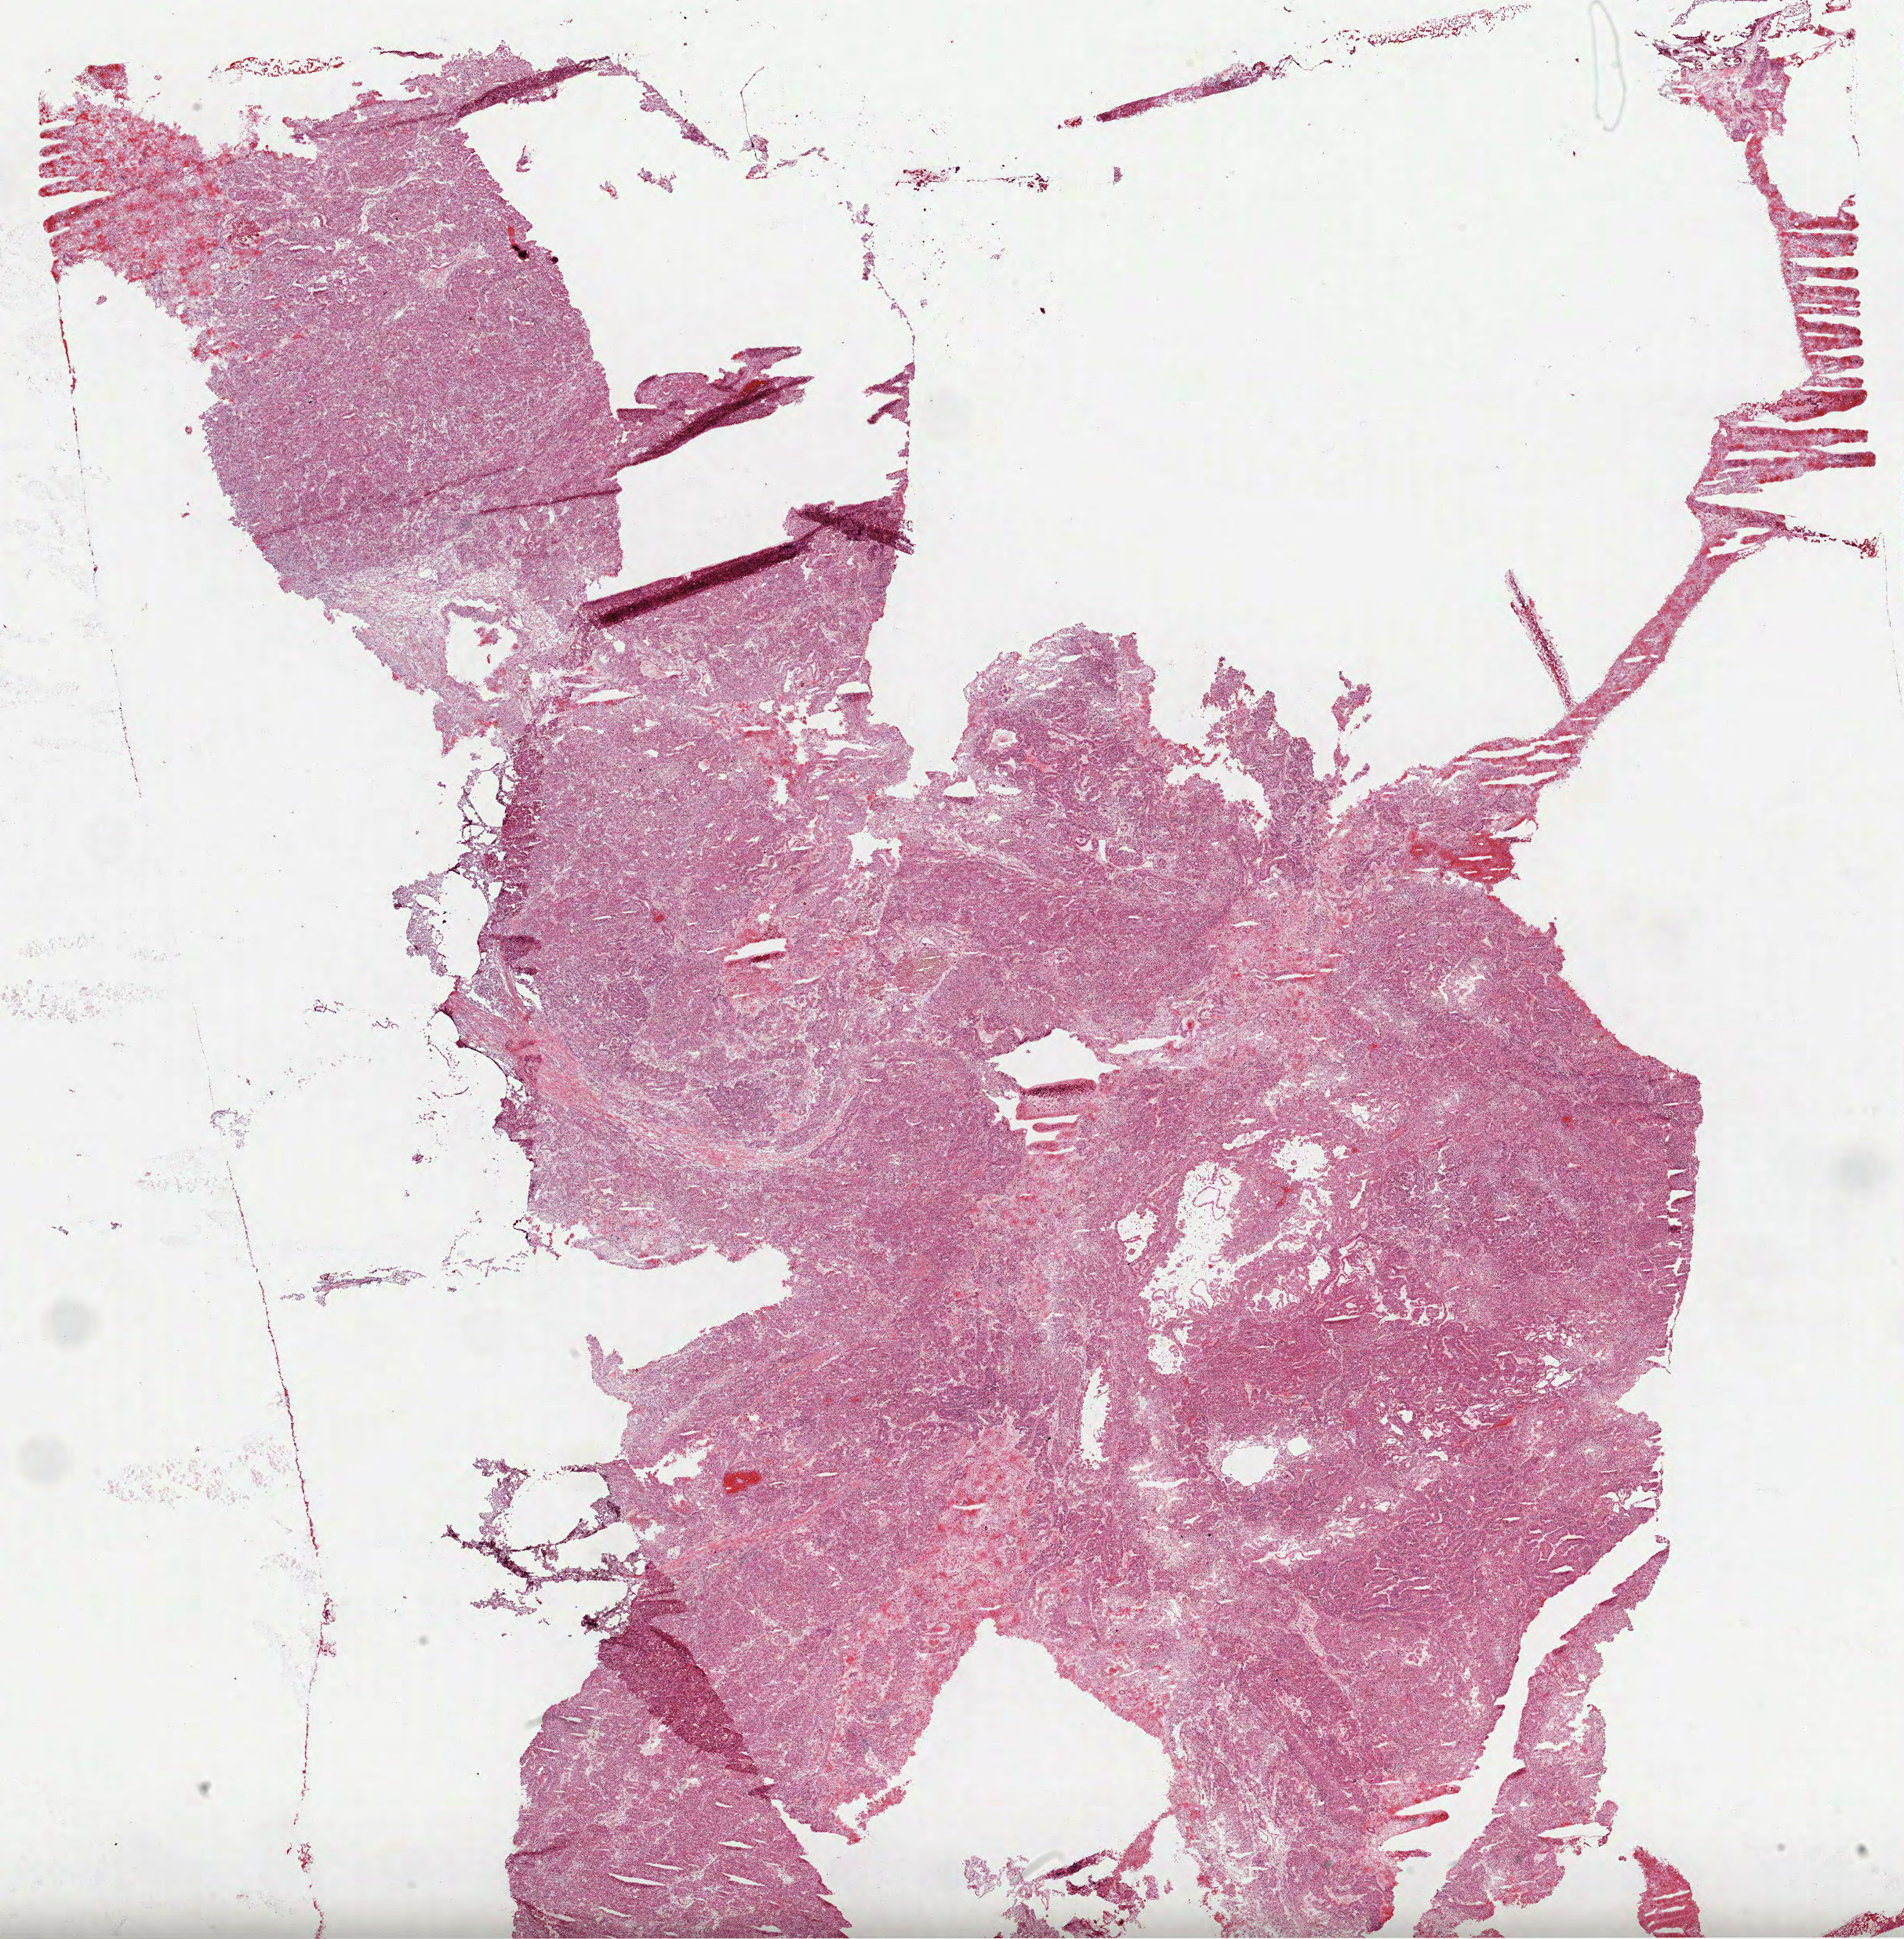
Digitized H&E tissue section (whole slide), low-resolution overview of the scanned area, about 19.6 x 19.9 mm (acquisition: 40x scan), frozen section from the top of the tissue portion, sample: primary tumour, kidney. Male patient; age at initial diagnosis 64 years. Pathologist review of this section (percent, as recorded): tumour cells 100%, tumour nuclei 85%, normal cells 0%, stromal cells 0%, necrosis 0%. Infiltration values recorded for this section: lymphocyte infiltration 2%, monocyte infiltration 5%, neutrophil infiltration 0%.
Pathologic diagnosis: Papillary adenocarcinoma, NOS. AJCC pathologic stage: III.